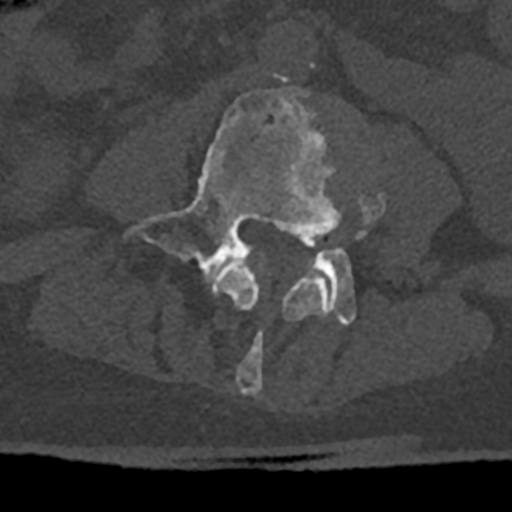
CT including the spine, one axial slice. Position 280 of 797 along the scan axis. Reconstruction kernel Br40s/3. 120 kVp. Bone window (W 1800 / L 400 HU). 0.5 mm slice thickness. 512 × 512 image matrix, field of view 160 × 160 mm. Patient: male, 74 years. From the clinical record (not read from this slice): primary cancer: renal; vertebrae with lytic lesions (as recorded): T10, L1, L2, L3, L4, L5.
Structures marked on this image (semi-automatically segmented with operator editing):
- L3 vertebra: box from (x=212, y=179) to (x=385, y=395) px
- L4 vertebra: (x=126, y=88)–(x=356, y=326)